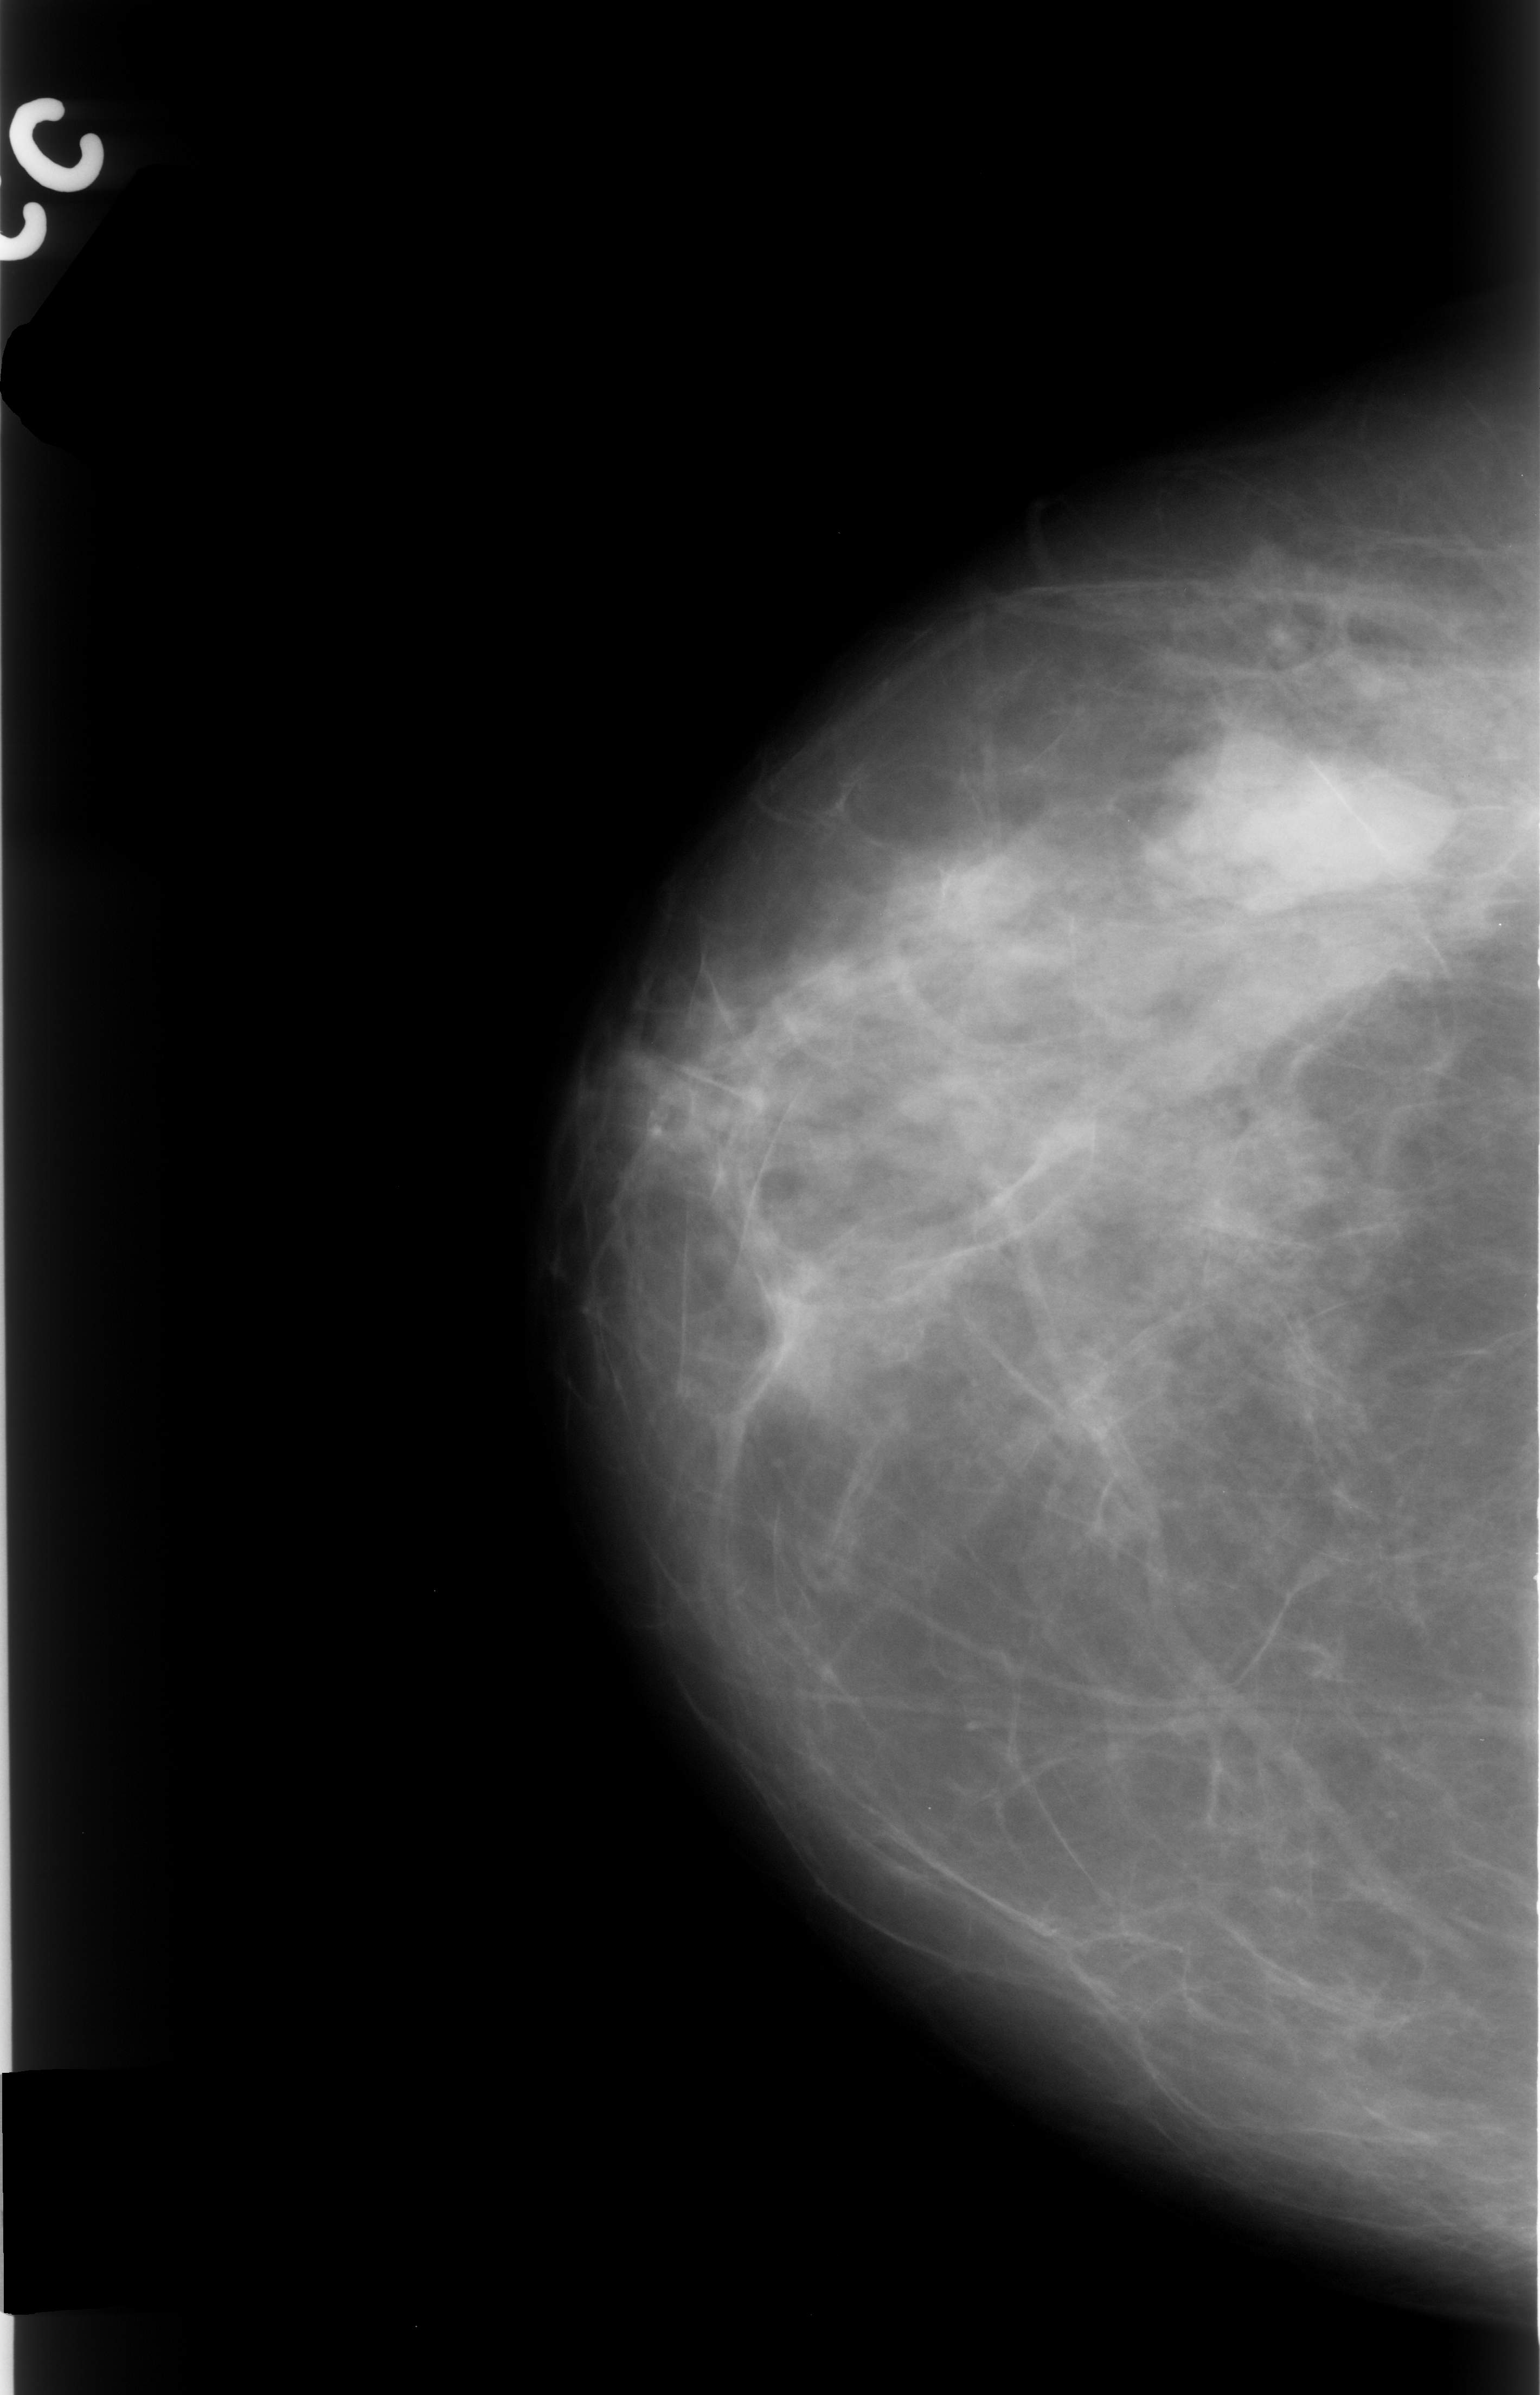
Digitized screen-film mammogram; right breast; CC view; BI-RADS breast density category 2 (scale 1–4); 1540 × 2395 image matrix.
Expert-marked regions of interest on this film, with their recorded descriptors:
- mass, shape lobulated, margins circumscribed; BI-RADS assessment category 4; subtlety rating 5 on a 1 (subtle) to 5 (obvious) scale; pathology result (as recorded, not read from the image): benign: box from (x=1138, y=689) to (x=1450, y=918) px